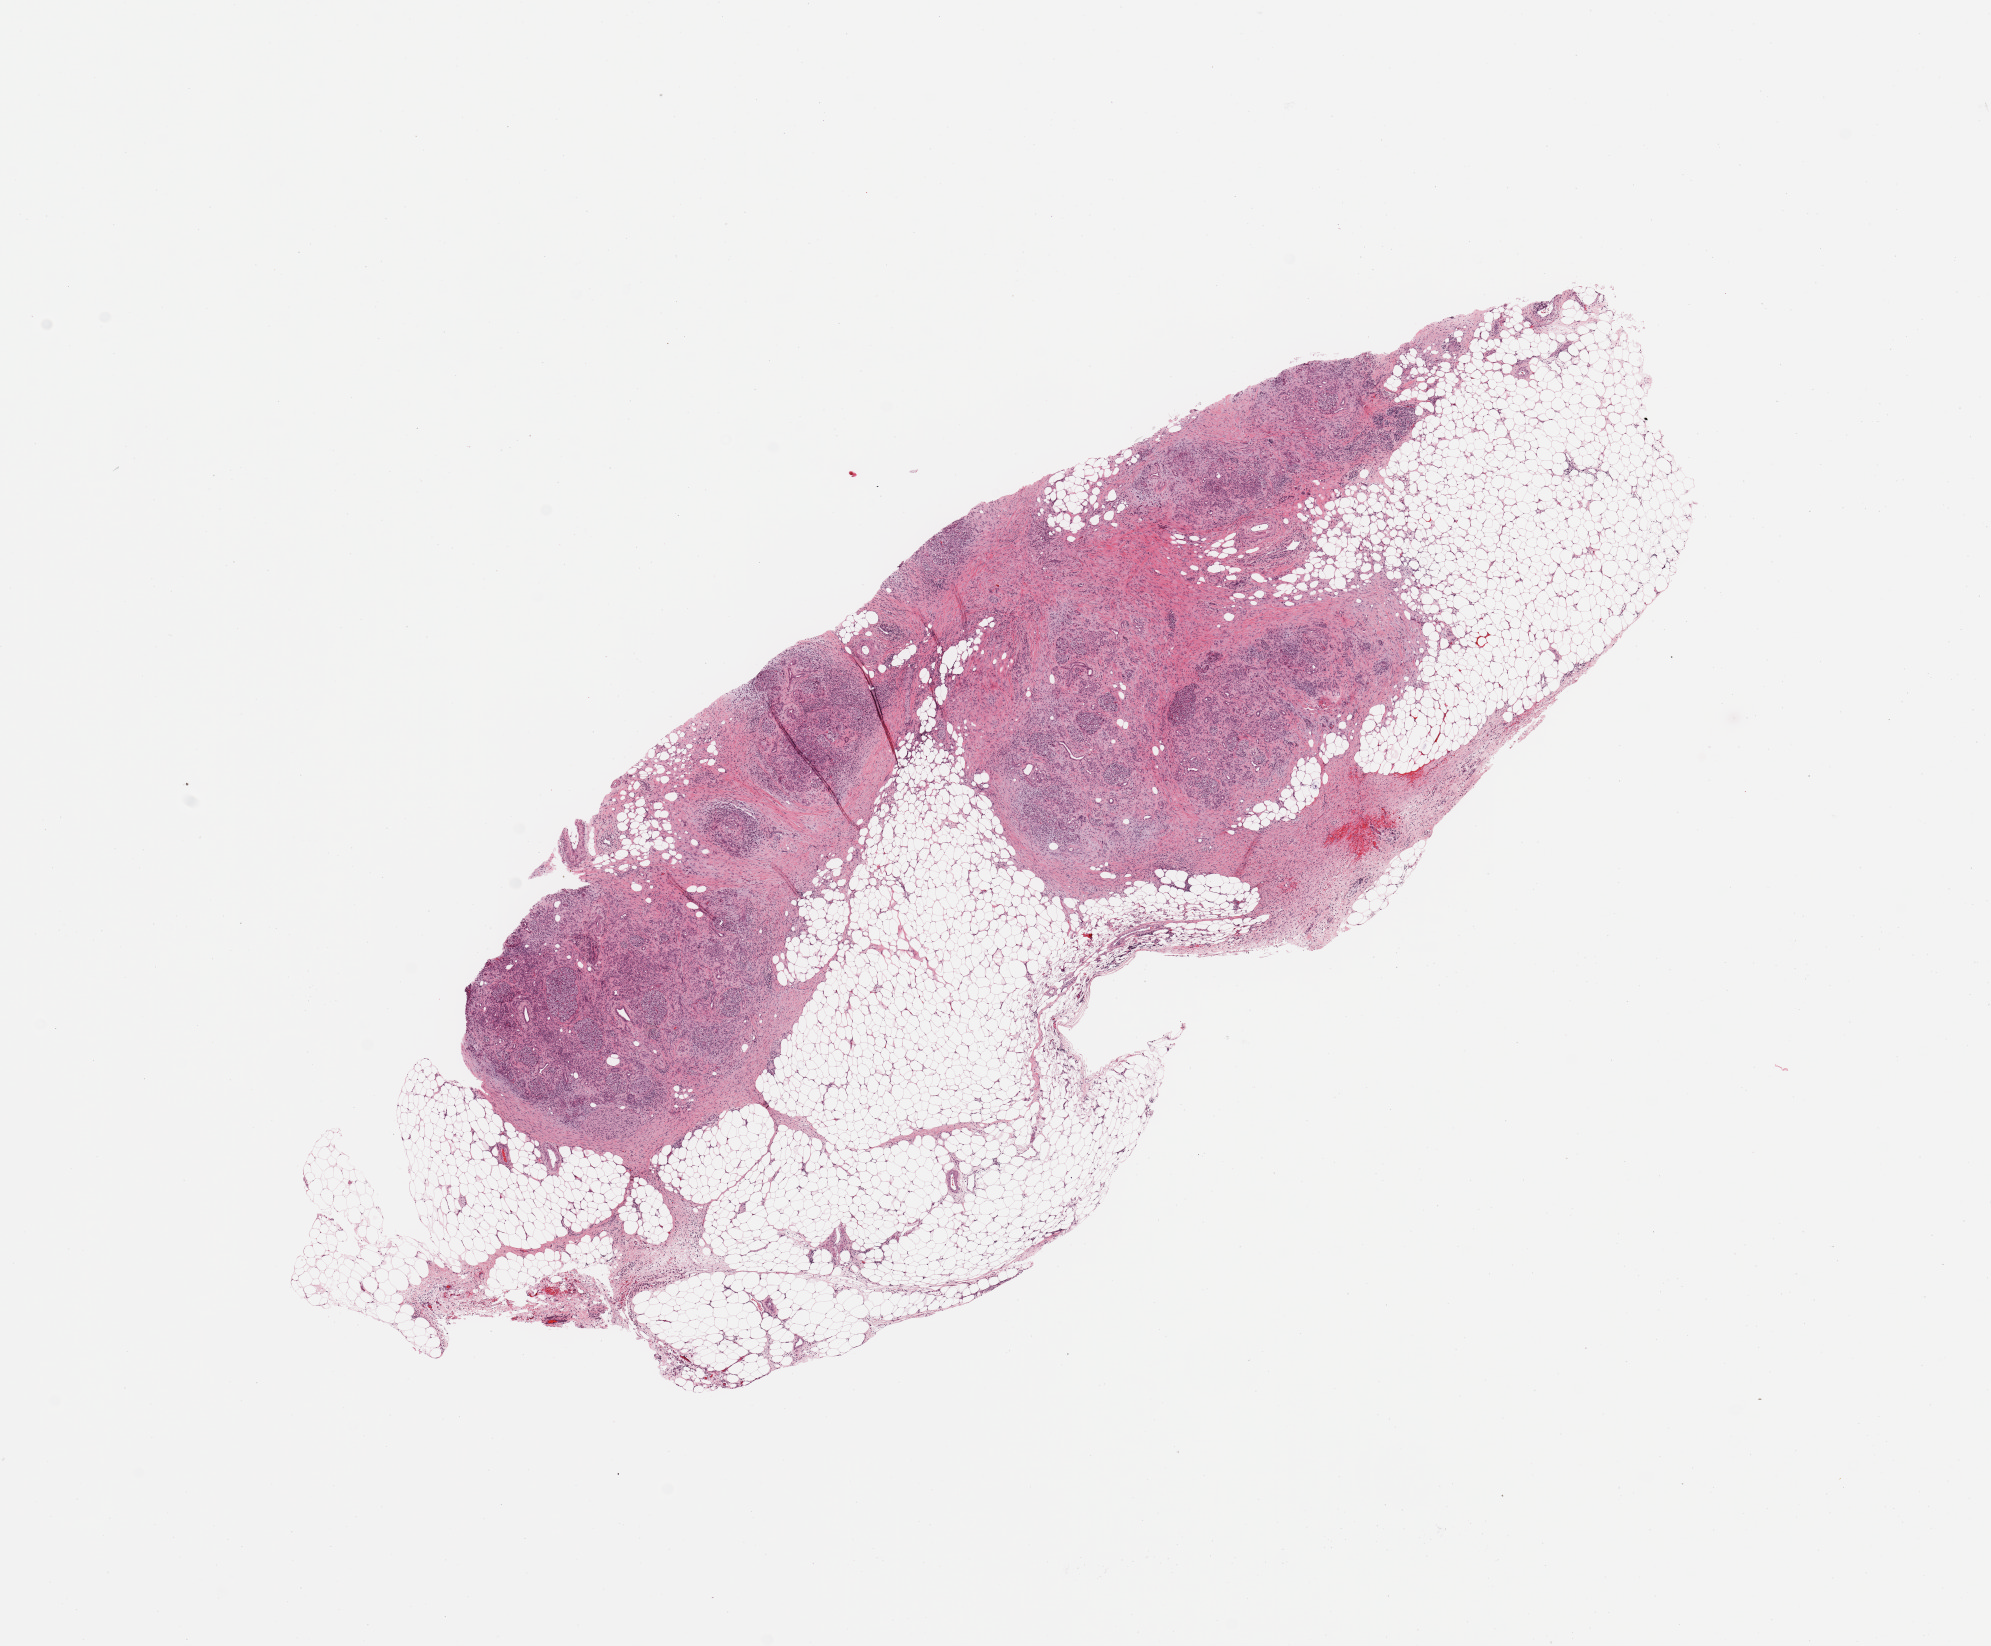
H&E-stained whole-slide image — whole scanned area (about 15.8 x 13.0 mm, acquisition: 20x scan) shown as a low-resolution overview. Normal (non-tumour) tissue sample, sampled site: pancreas. 74-year-old male patient.
* this section: normal (non-tumour) tissue from the same patient
* patient diagnosis: Infiltrating duct carcinoma, NOS